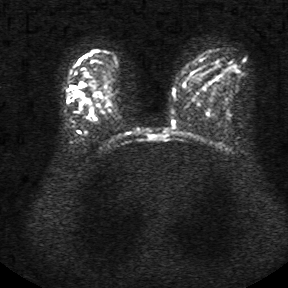
Breast MRI, one axial slice. Slice 25 of 34 in the series (ordered by position). Diffusion-weighted series; image 2 of 4 stored at this slice position (different b-values; order by instance number). 1.5 T. 288 × 288 image matrix, field of view 340 × 340 mm. Female patient.
Outlined on this slice (outlined manually by an expert reader):
- tumour on diffusion-weighted imaging: bounding box <80,83,86,100> (left, top, right, bottom; pixels)